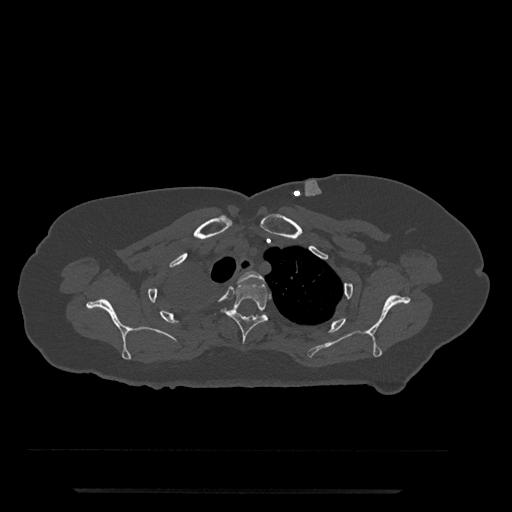
CT including the spine, one axial slice; position 633 of 797 along the scan axis; reconstruction kernel Br40s/3; bone window (W 1800 / L 400 HU); 0.5 mm slice thickness; 512 × 512 image matrix, field of view 440 × 440 mm. Female patient, age 51 years. Case-level facts recorded for this patient, not image findings: primary cancer: neuro.
Annotated regions visible in this slice (semi-automatically segmented with operator editing):
- T2 vertebra: bounding box <238,271,264,282> (left, top, right, bottom; pixels)
- T3 vertebra: <214,282,268,344>
- T4 vertebra: <234,310,239,314>